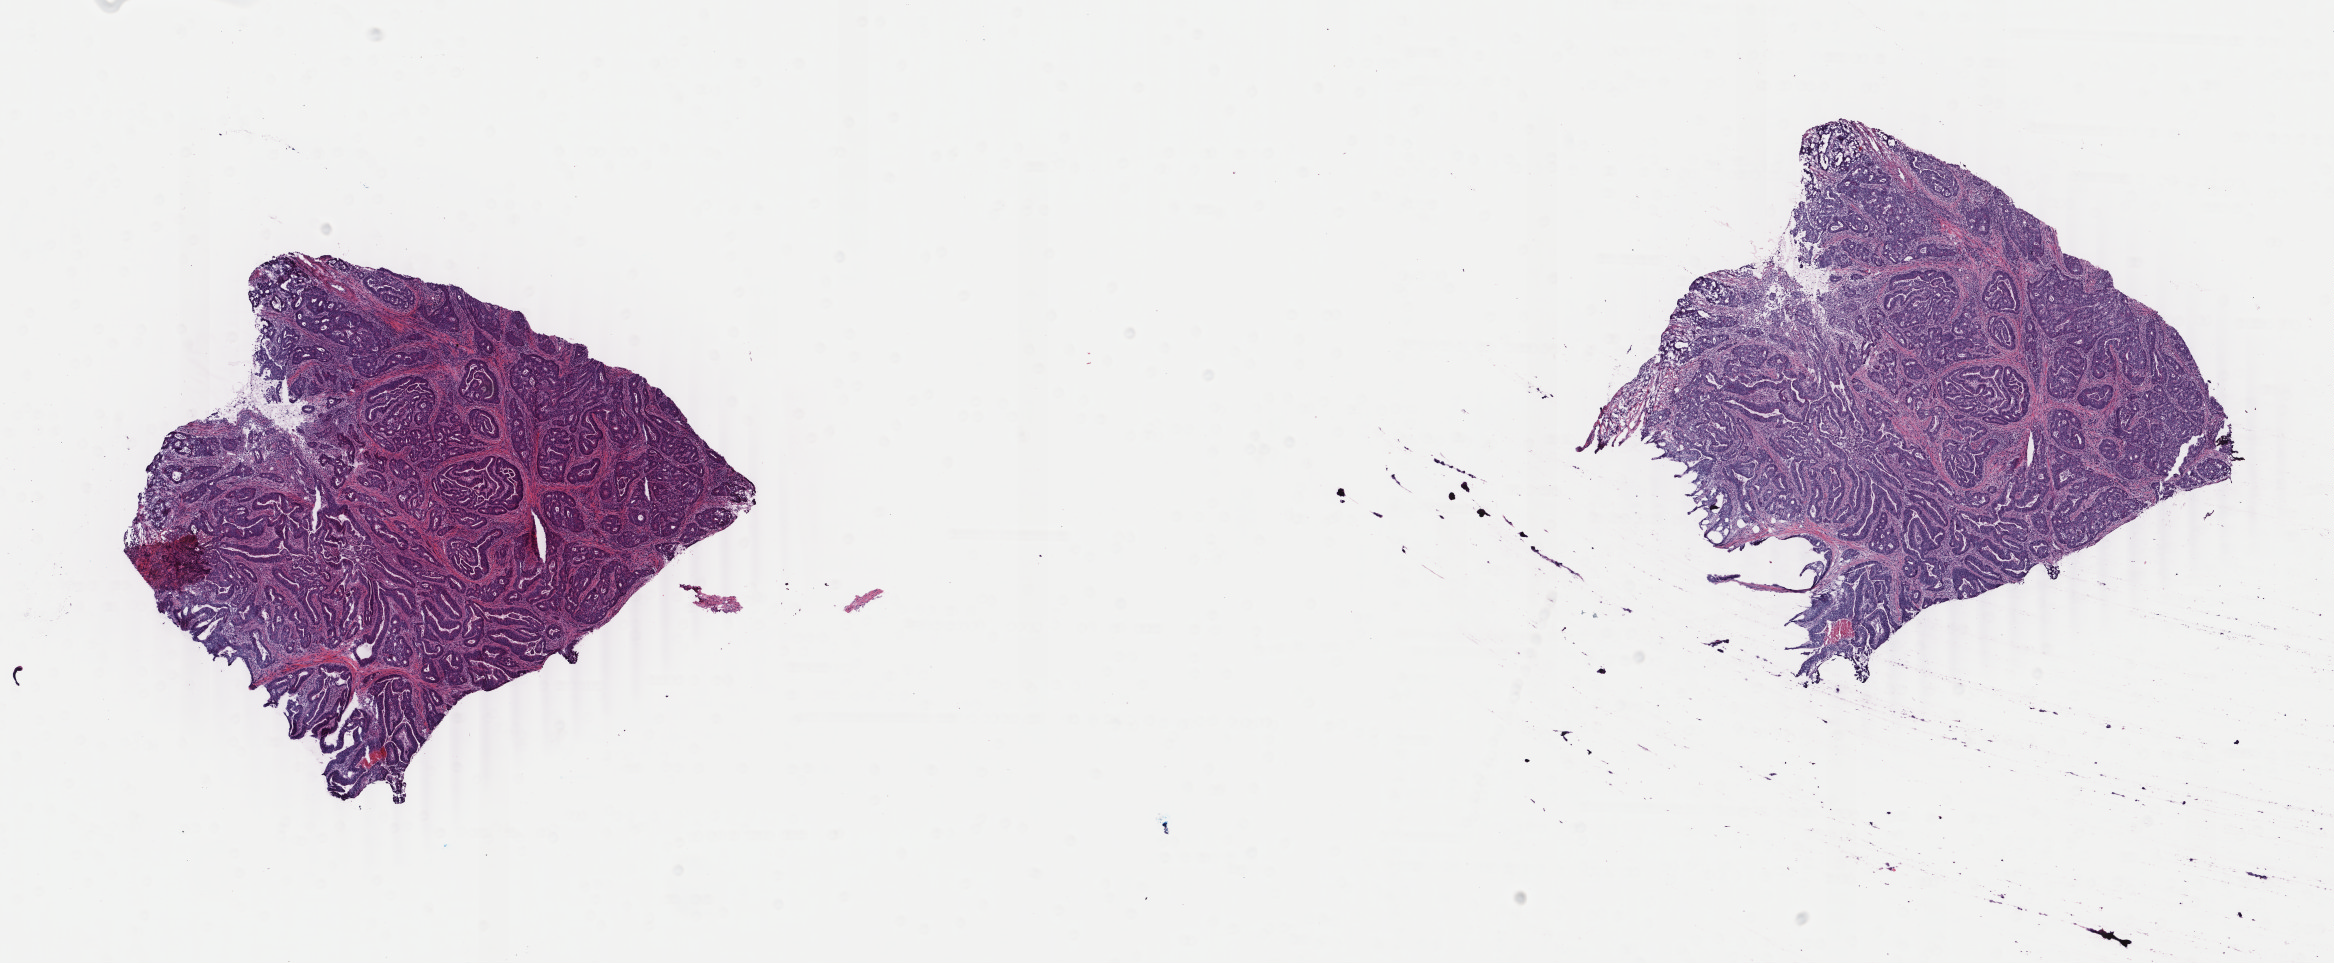
Digitized Hematoxylin and eosin (H&E) stained tissue section (whole slide), whole scanned area (about 18.6 x 7.7 mm) shown as a low-resolution overview. Frozen section. Primary tumour sample from the colon. Male, age 70 years at initial diagnosis. Composition of this section per pathologist review: tumour cells 78%, tumour nuclei 80%, normal cells 2%, stromal cells 18%, necrosis 2%. Inflammatory infiltration, as recorded: lymphocyte infiltration 10%, monocyte infiltration 1%, neutrophil infiltration 1%.
* lymph nodes positive (case pathology): 0 of 28 examined
* pathologic diagnosis: Adenocarcinoma, NOS (ascending colon)
* AJCC pathologic stage: I (6th edition)